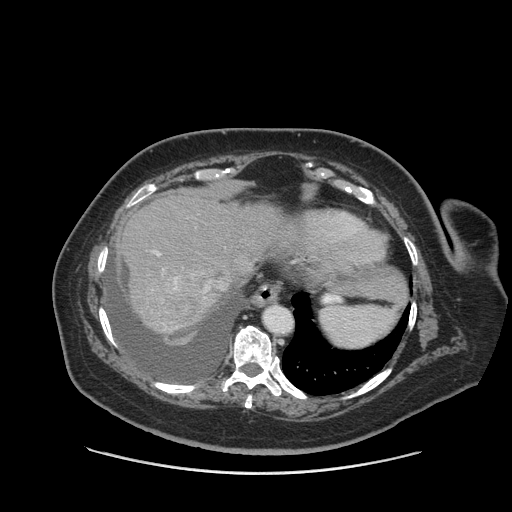
Contrast-enhanced abdominal CT (liver protocol), one axial slice; position 71 of 91 along the scan axis; reconstruction kernel STANDARD; 140 kVp; soft-tissue window (W 400 / L 40 HU); 2.5 mm slice thickness; 512 × 512 image matrix. Case-level facts recorded for this patient, not image findings: diagnosis: hepatocellular carcinoma (patient treated with transarterial chemoembolisation; whether this scan precedes or follows treatment is not stated here); TNM stage (as recorded): Stage-I; Child-Pugh class: A; tumour differentiation: well differentiated; tumour nodularity: uninodular.
Outlined on this slice (semi-automatically segmented with operator editing):
- abdominal aorta: bounding box <265,307,292,333> (left, top, right, bottom; pixels)
- liver parenchyma outside the tumour (the mass and vessels are separate outlines, so this box may not span the whole liver): <118,190,294,334>
- mass: <148,294,205,328>
- liver vessels: <153,251,177,290>